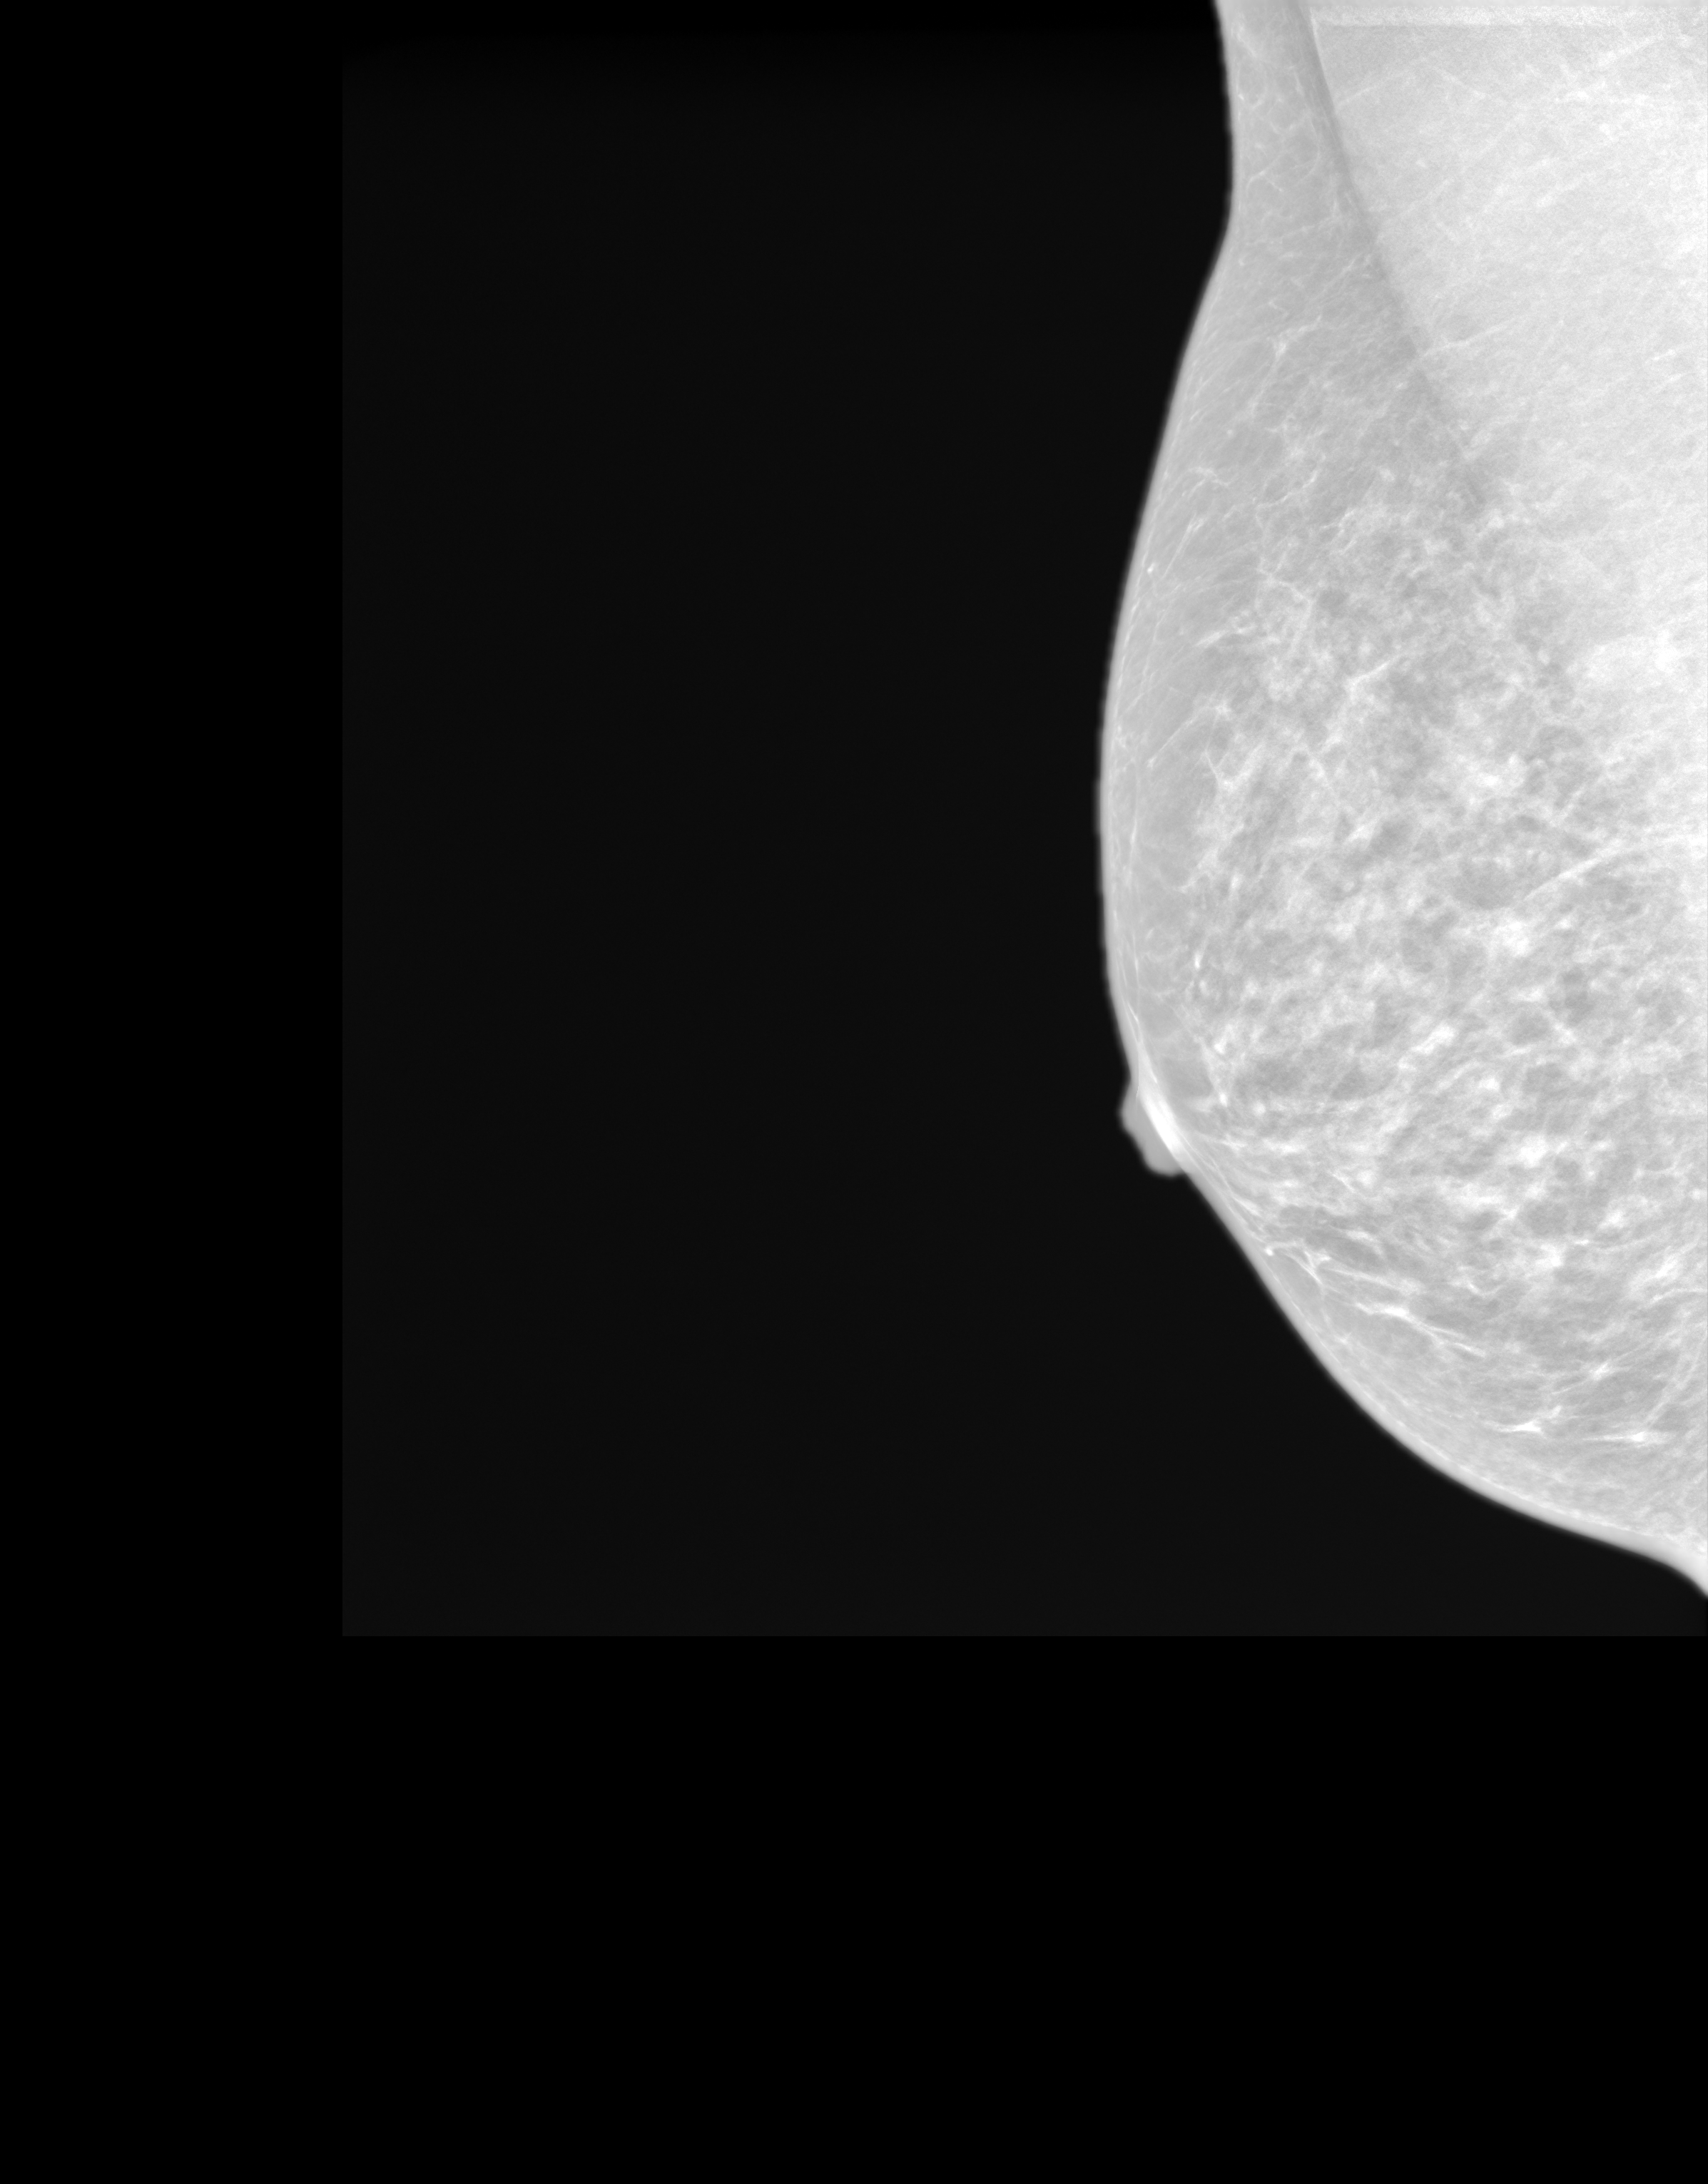
Screening examination. Patient aged 70 years (female).
Image type: synthesized 2-D view from tomosynthesis. Breast: right. Projection: medio-lateral oblique projection.